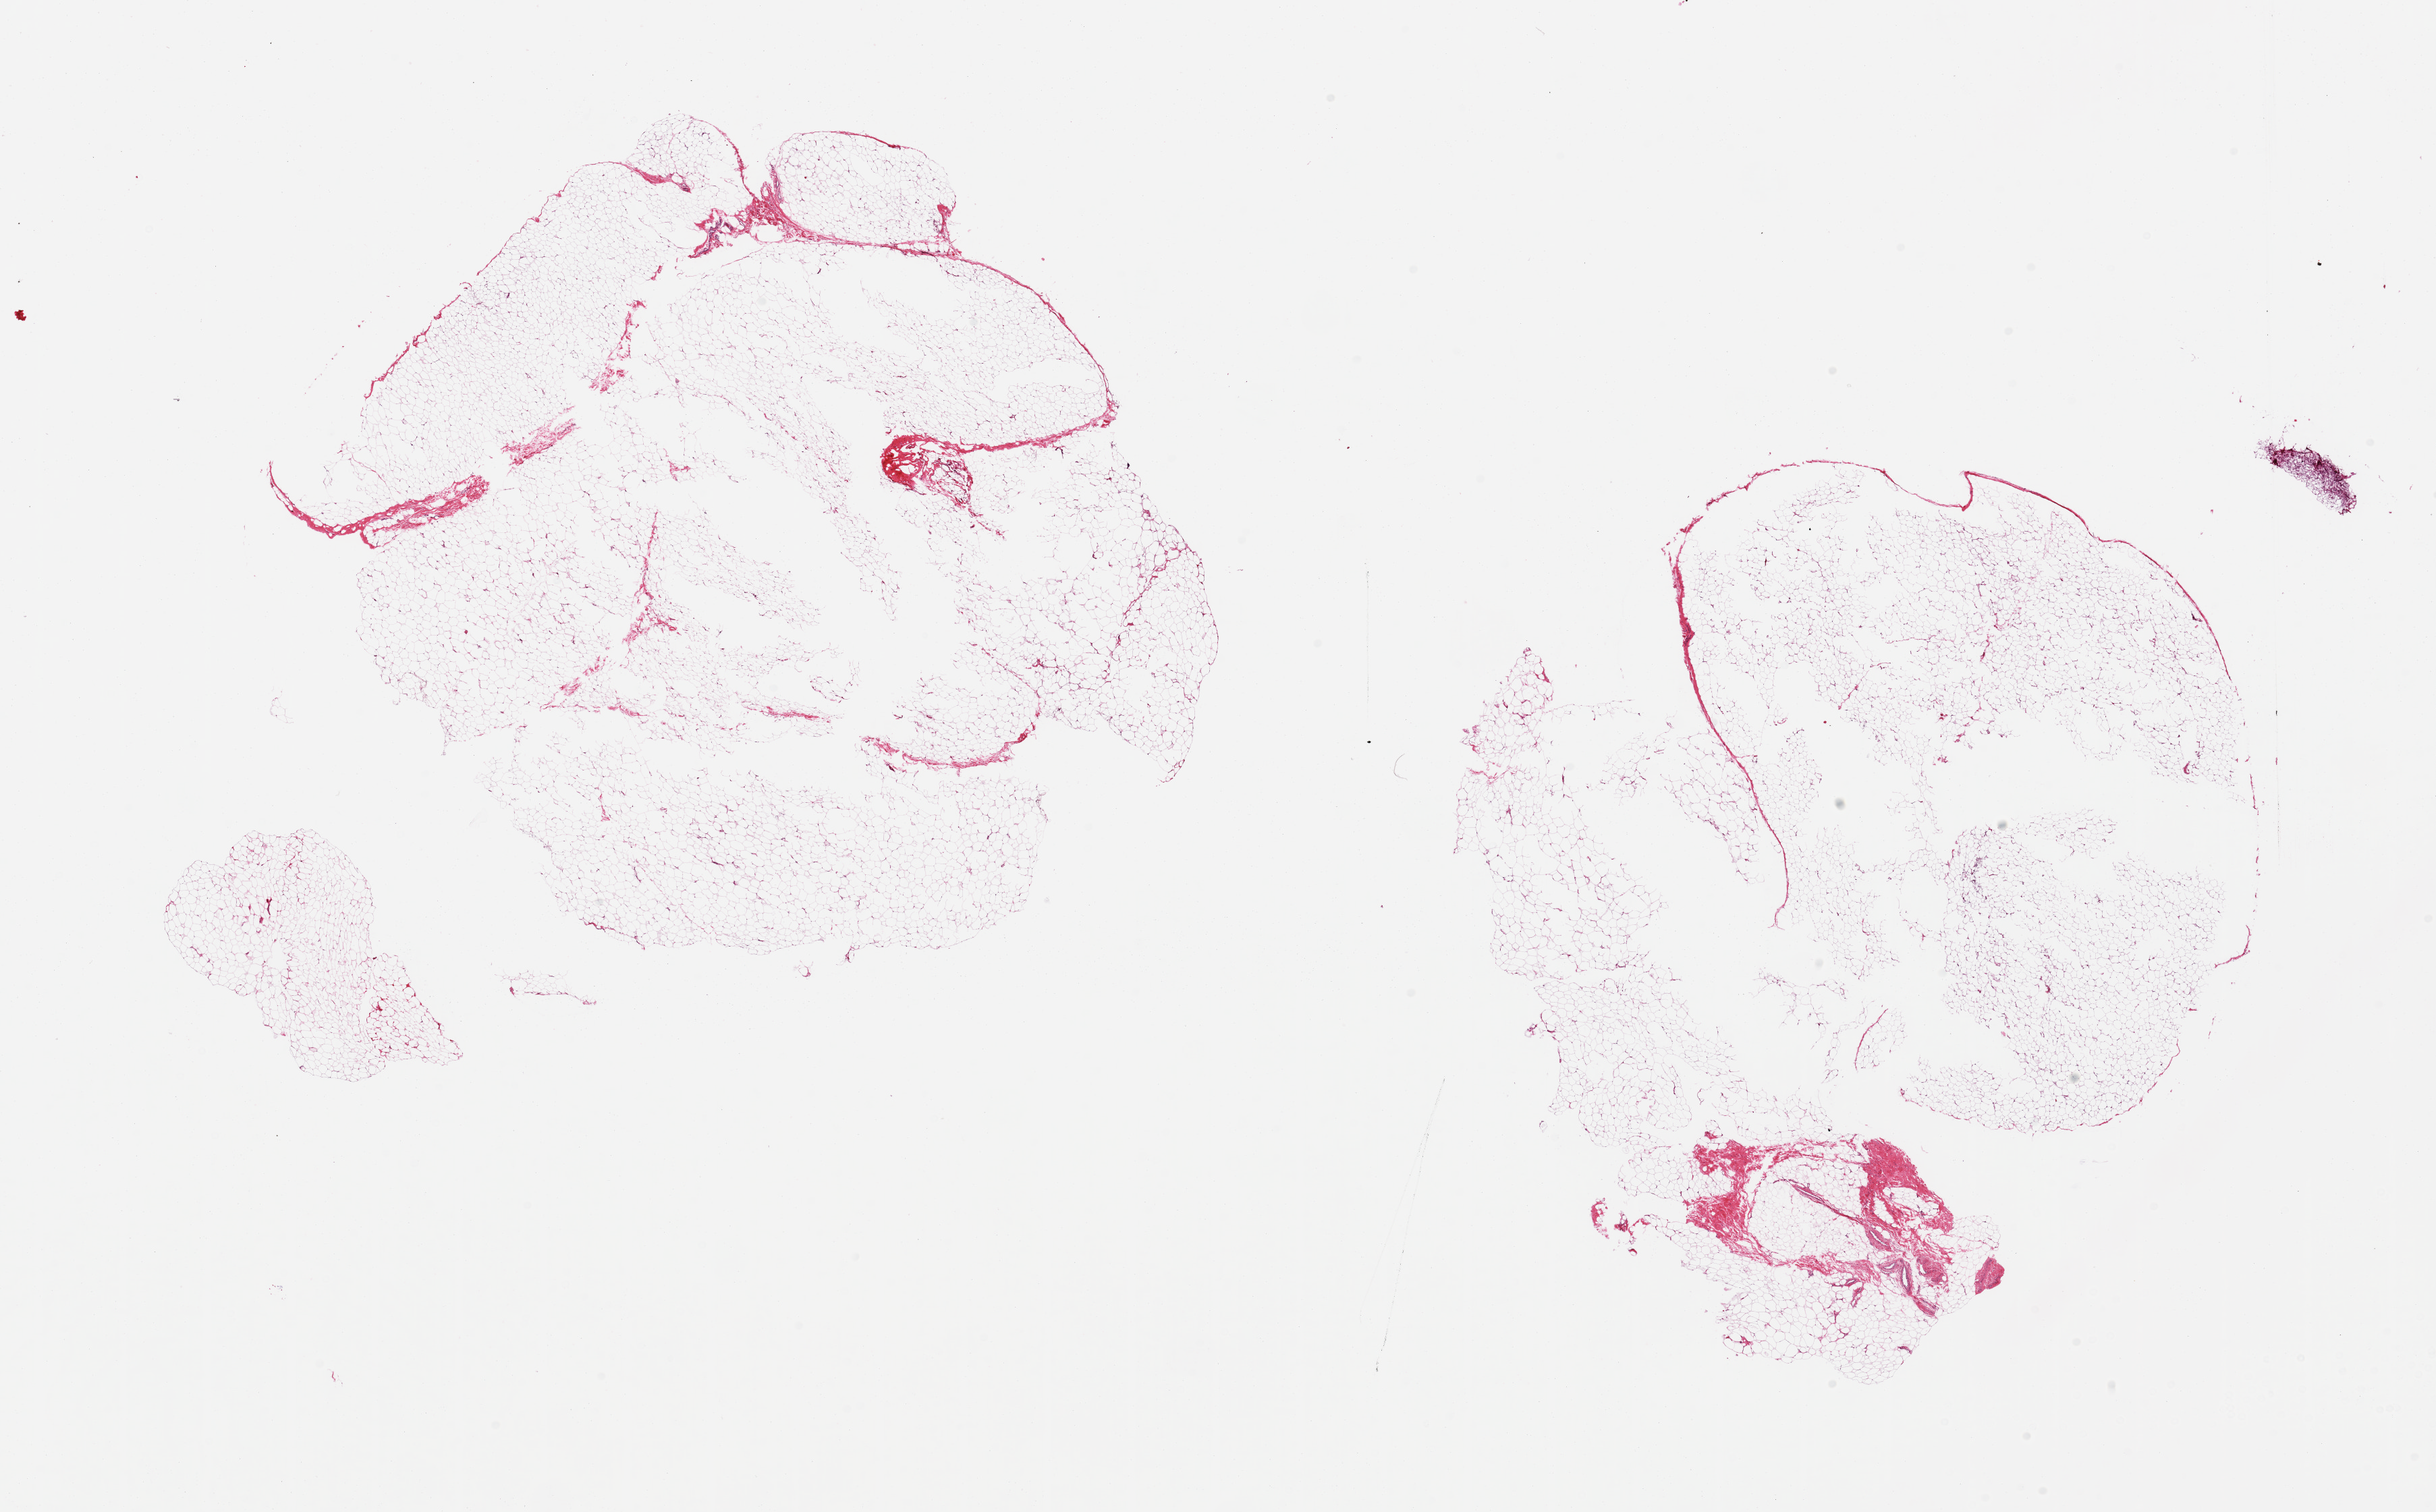
Whole-slide image, haematoxylin and eosin stain — whole scanned area (about 28.5 x 17.7 mm, acquisition: 20x scan) shown as a low-resolution overview; PAXgene-fixed, paraffin-embedded tissue; sampled site (target tissue): breast; tissue donor sample. Donor: male.
Pathologist's review note for this sample: 2 pieces. mainly adipose, trace fibrous elements.